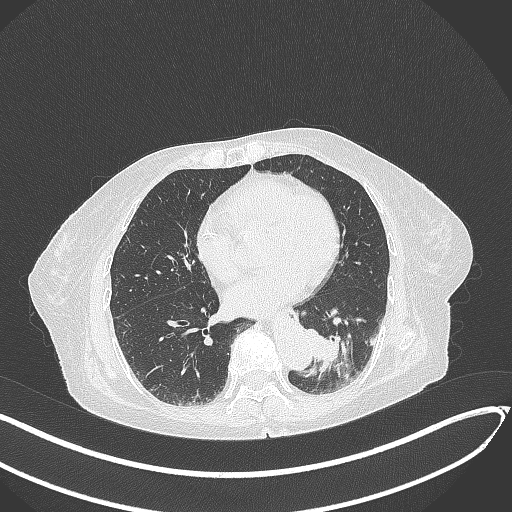
Chest CT, one axial slice; slice 95 of 324 in the series (ordered by position); 120 kVp; lung window (W 1500 / L -600 HU); 1 mm slice thickness; 512 × 512 image matrix, field of view 400 × 400 mm. Female patient, age 82 years. Case-level facts recorded for this patient, not image findings: clinical TNM (as recorded): T1b N0 M1.
Outlined on this slice (rectangle marked by the reading radiologist):
- lung tumour (recorded histology: adenocarcinoma): box from (x=304, y=323) to (x=347, y=375) px